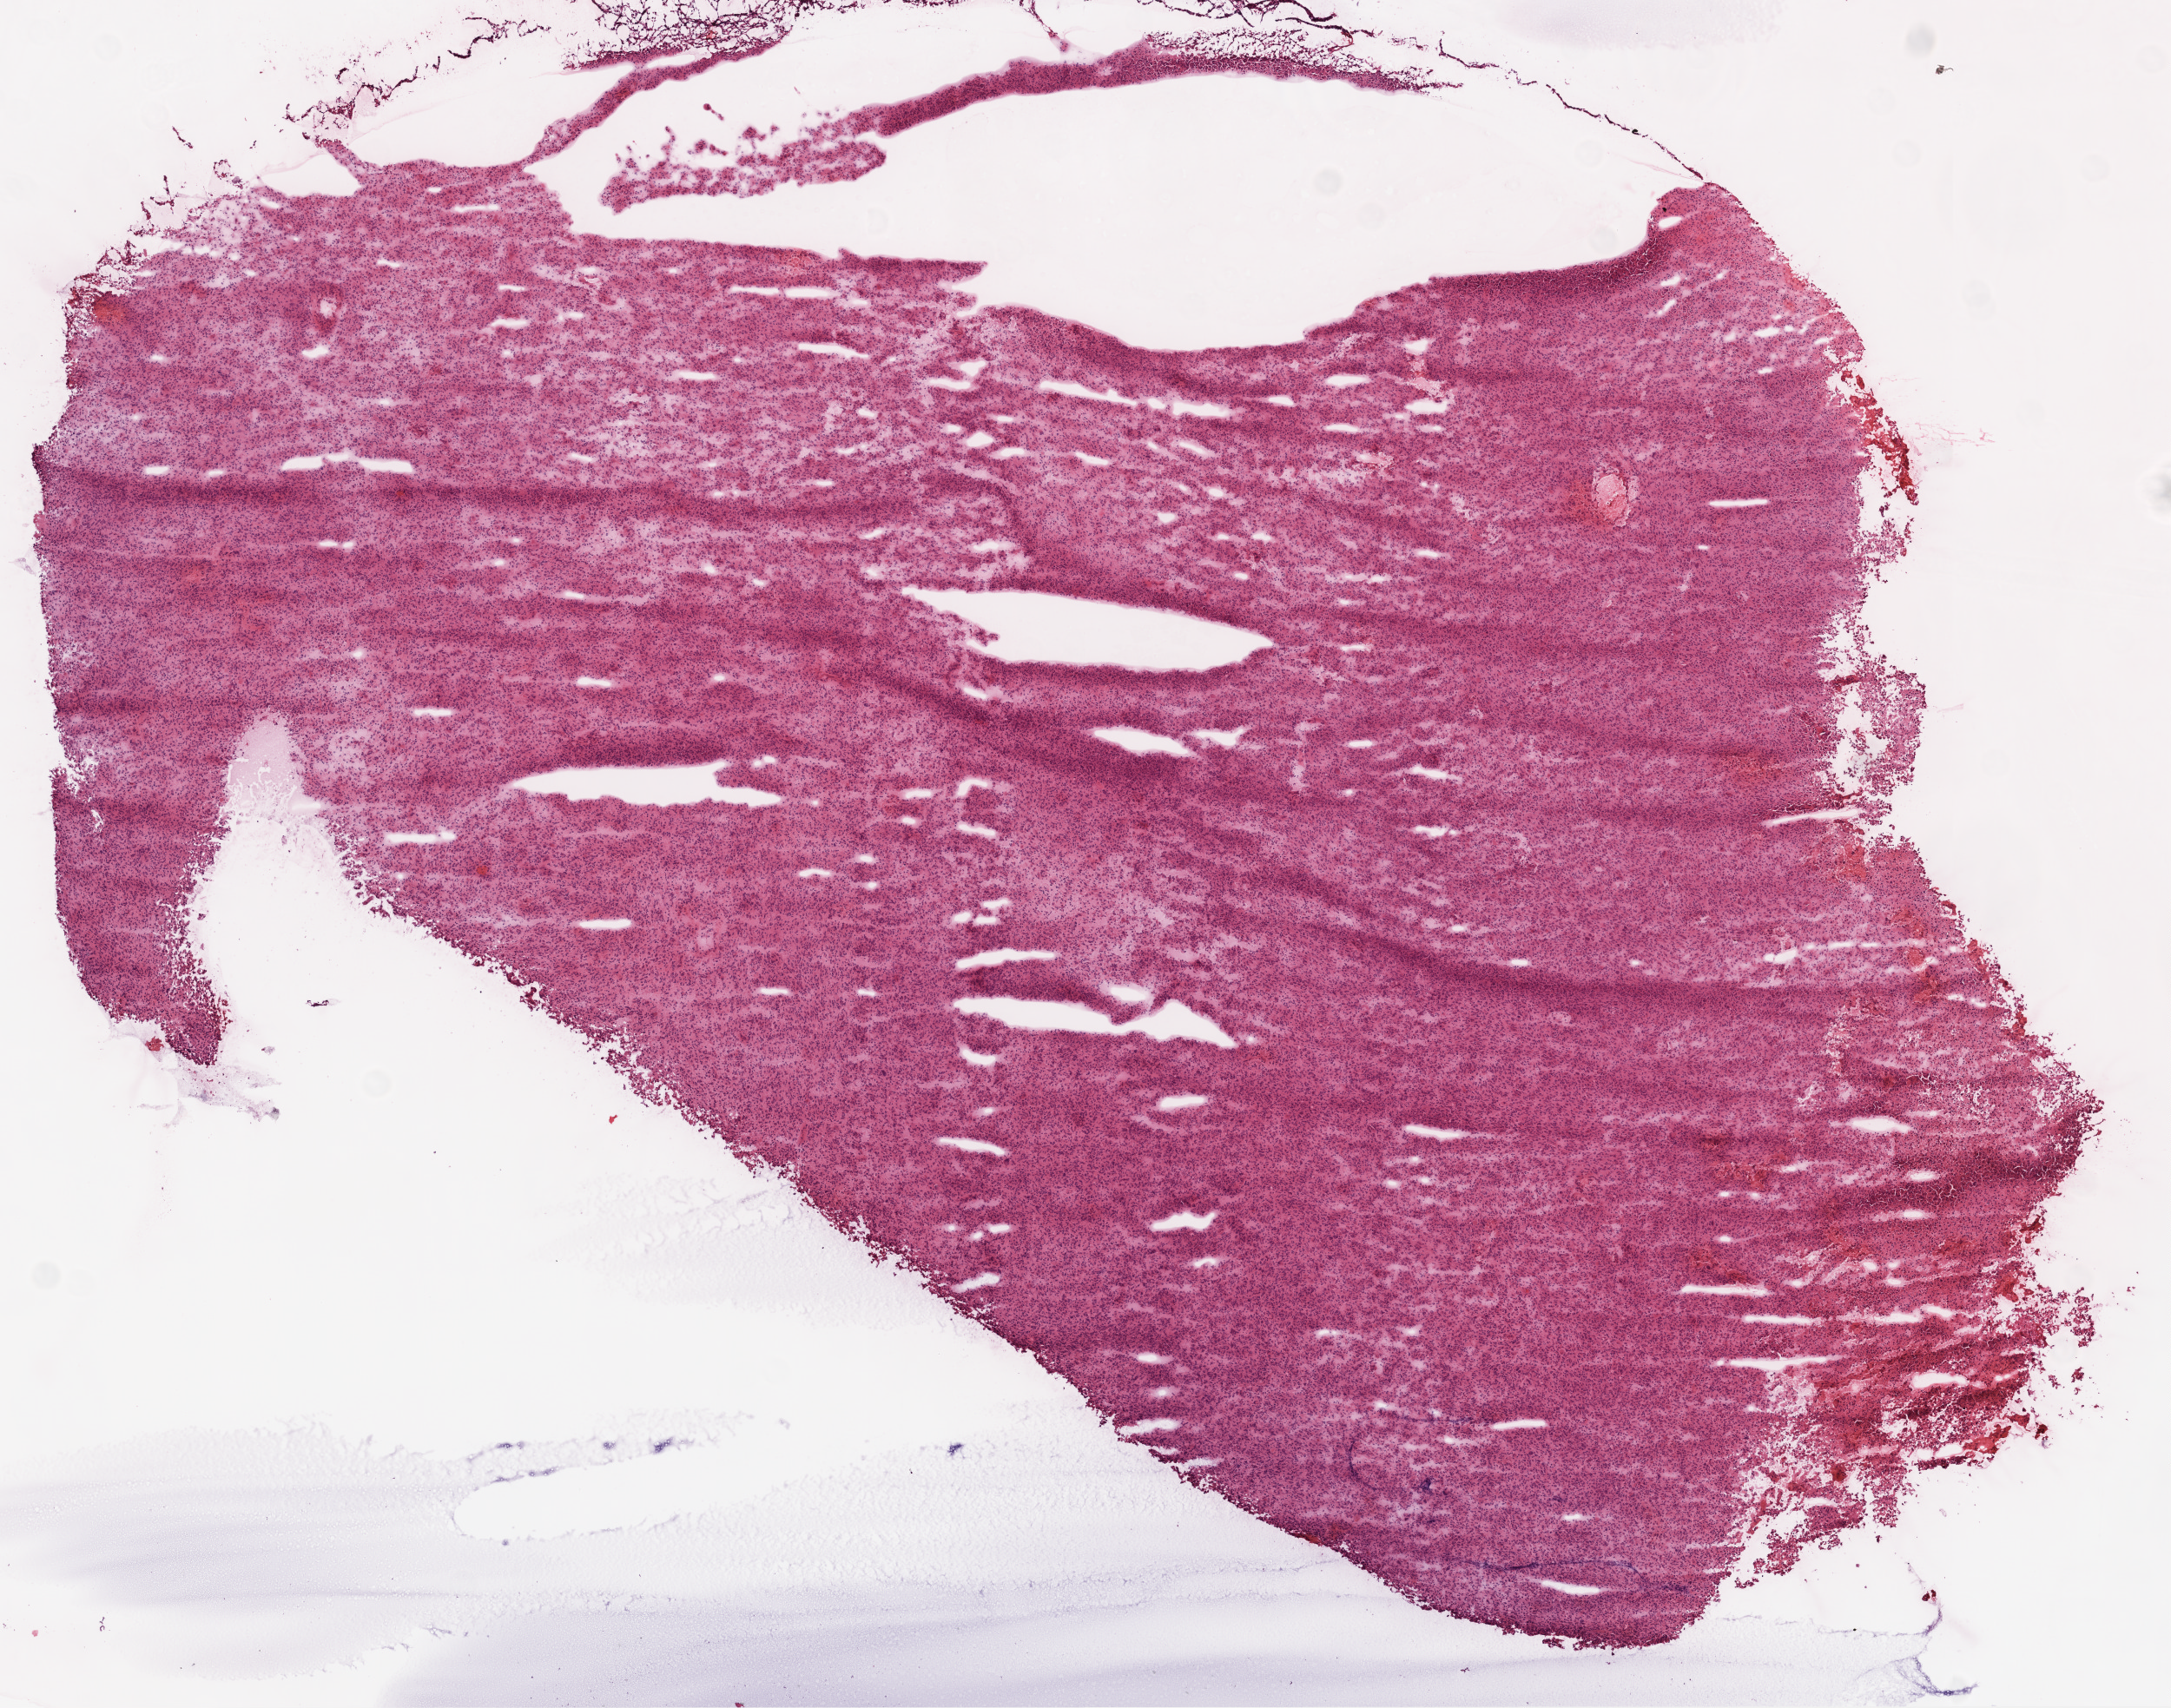
Digitized H&E tissue section (whole slide), low-resolution overview of the scanned area, about 10.0 x 7.9 mm (slide scanned at 20x), frozen section, primary tumour sample from the brain. Female patient; age at initial diagnosis 75 years.
Diagnosis: Glioblastoma.